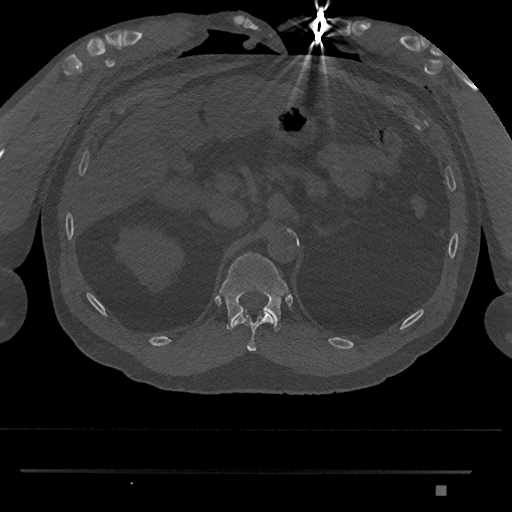
CT including the spine, one axial slice; slice 910 of 1134 in the series (ordered by position); reconstruction kernel Br40s/3; bone window (W 1800 / L 400 HU); 0.5 mm slice thickness; 512 × 512 image matrix, field of view 429 × 429 mm. Male patient, age 65 years. Case-level facts recorded for this patient, not image findings: primary cancer: prostate.
Outlined on this slice (semi-automatically segmented with operator editing):
- T11 vertebra: bounding box [x1, y1, x2, y2] px = [234, 311, 273, 352]
- T12 vertebra: [219, 252, 289, 332]